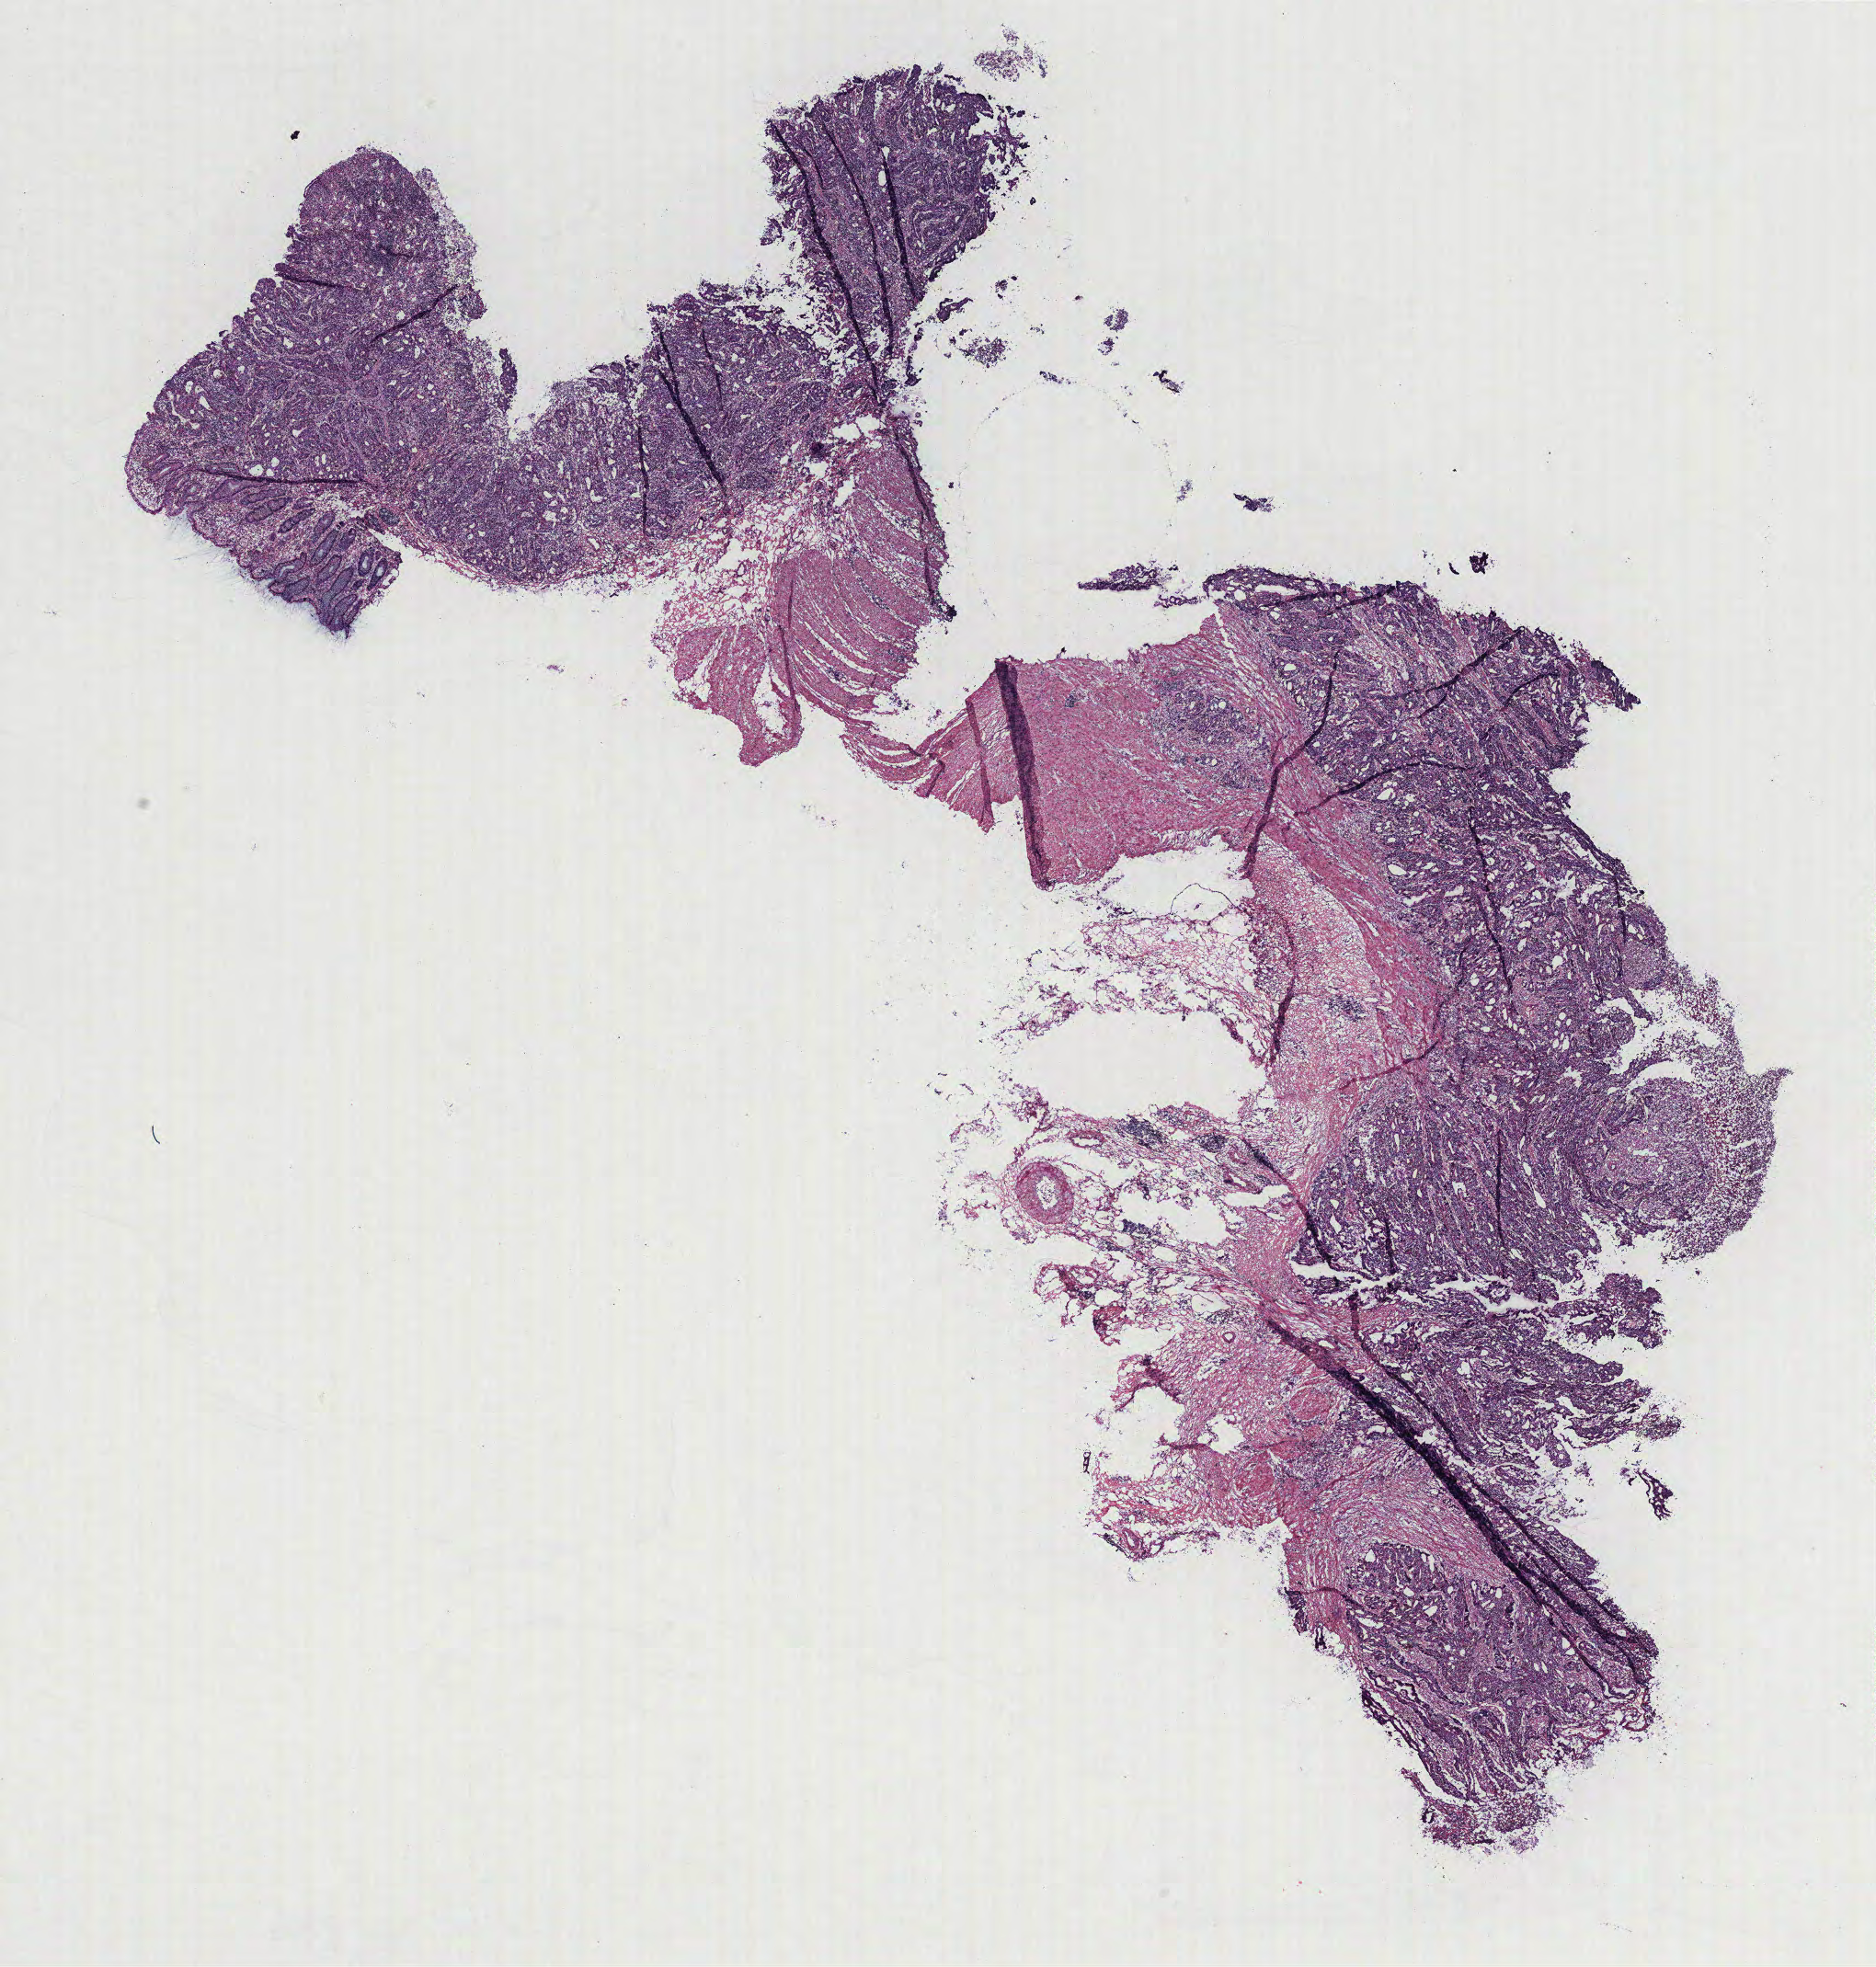
Digitized Hematoxylin and eosin (H&E) stained tissue section (whole slide), low-resolution overview of the scanned area, about 16.3 x 17.1 mm (slide scanned at 40x). Colon, tumour tissue. Male, 57 y/o.
- diagnosis: Adenocarcinoma, NOS
- primary tumour site (as recorded): colon
- AJCC pathologic stage: IIIB